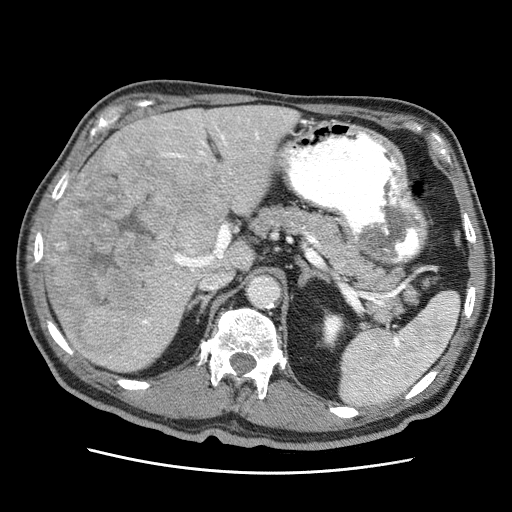
Contrast-enhanced abdominal CT (liver protocol), one axial slice; slice 29 of 75 in the series (ordered by position); 120 kVp; soft-tissue window (W 400 / L 40 HU); 2.5 mm slice thickness; 512 × 512 image matrix. Case-level facts recorded for this patient, not image findings: diagnosis: hepatocellular carcinoma (patient treated with transarterial chemoembolisation; whether this scan precedes or follows treatment is not stated here); TNM stage (as recorded): Stage-IIIA; Child-Pugh class: A.
Outlined on this slice (semi-automatic segmentation, software-assisted and operator-edited):
- liver parenchyma outside the tumour (the mass and vessels are separate outlines, so this box may not span the whole liver): bounding box (x1, y1, x2, y2) in pixels: (44, 104, 298, 372)
- mass: (48, 136, 237, 361)
- liver vessels: (134, 116, 285, 354)